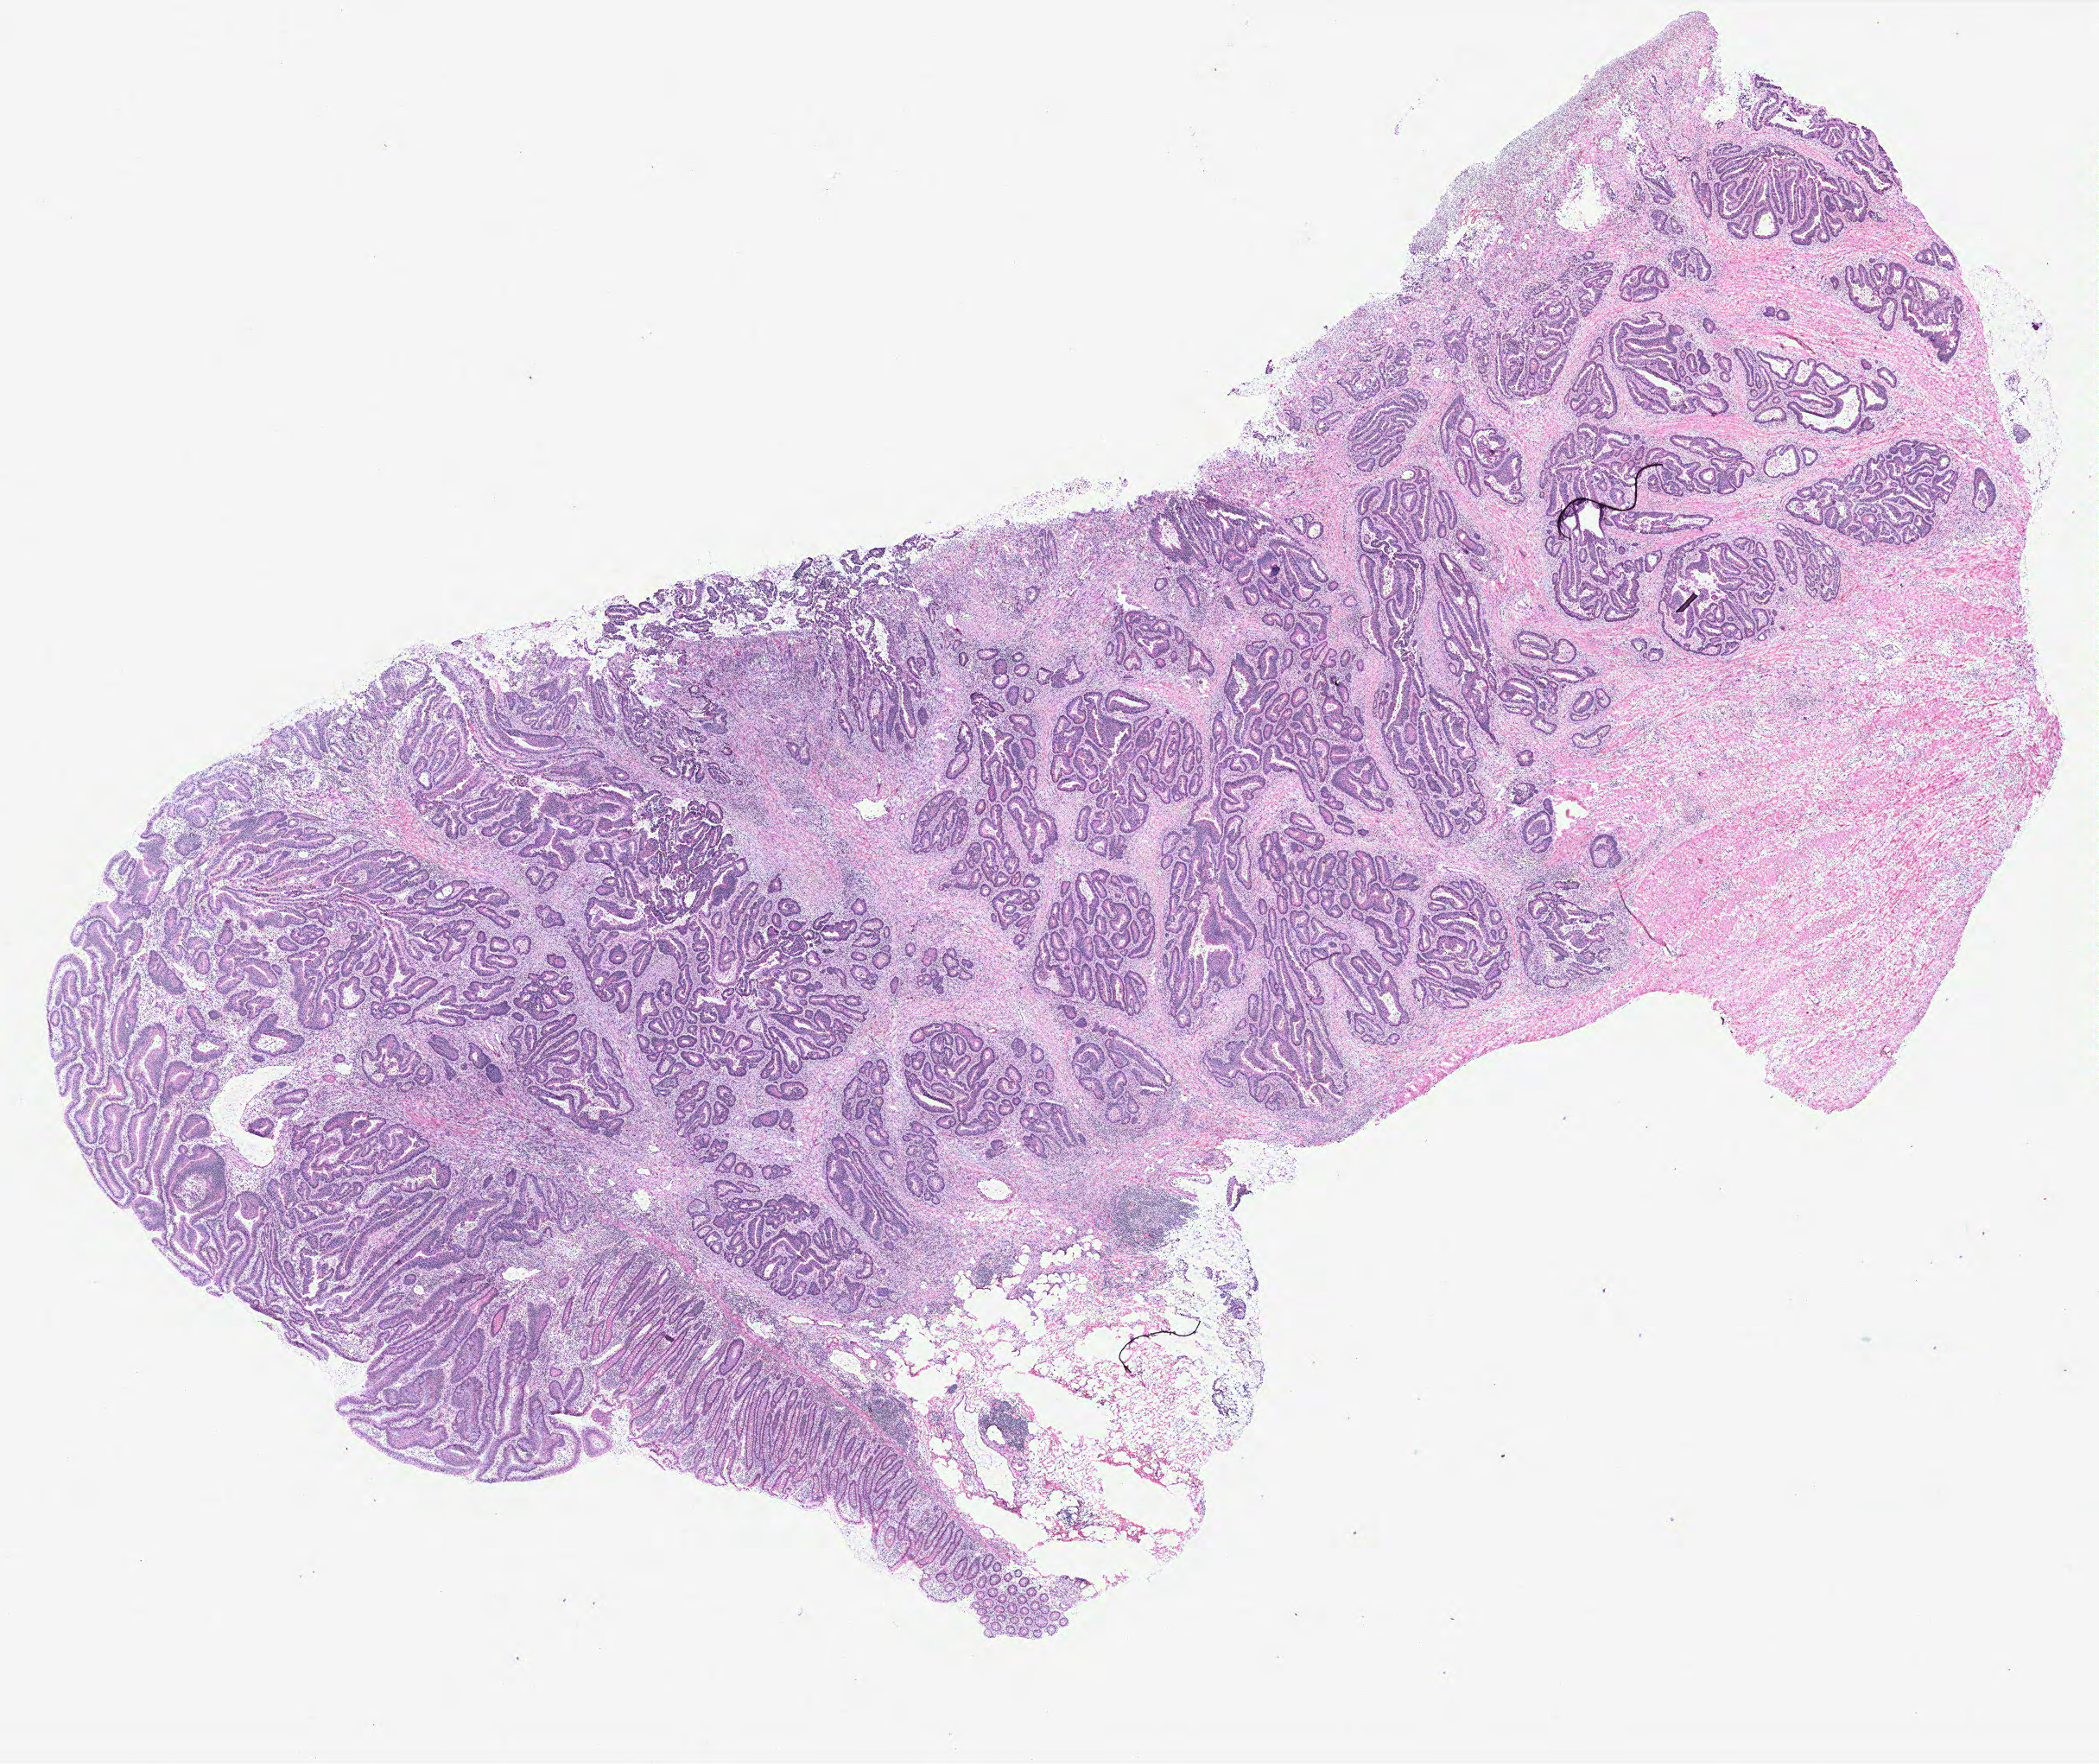
Whole-slide histology image, H&E, shown as a low-resolution overview of the whole scanned area (about 19.4 x 16.3 mm, acquisition: 40x scan); colon, normal (non-tumour) tissue. 66-year-old male patient.
* this section: normal (non-tumour) tissue from the same patient
* patient diagnosis: Adenocarcinoma, NOS